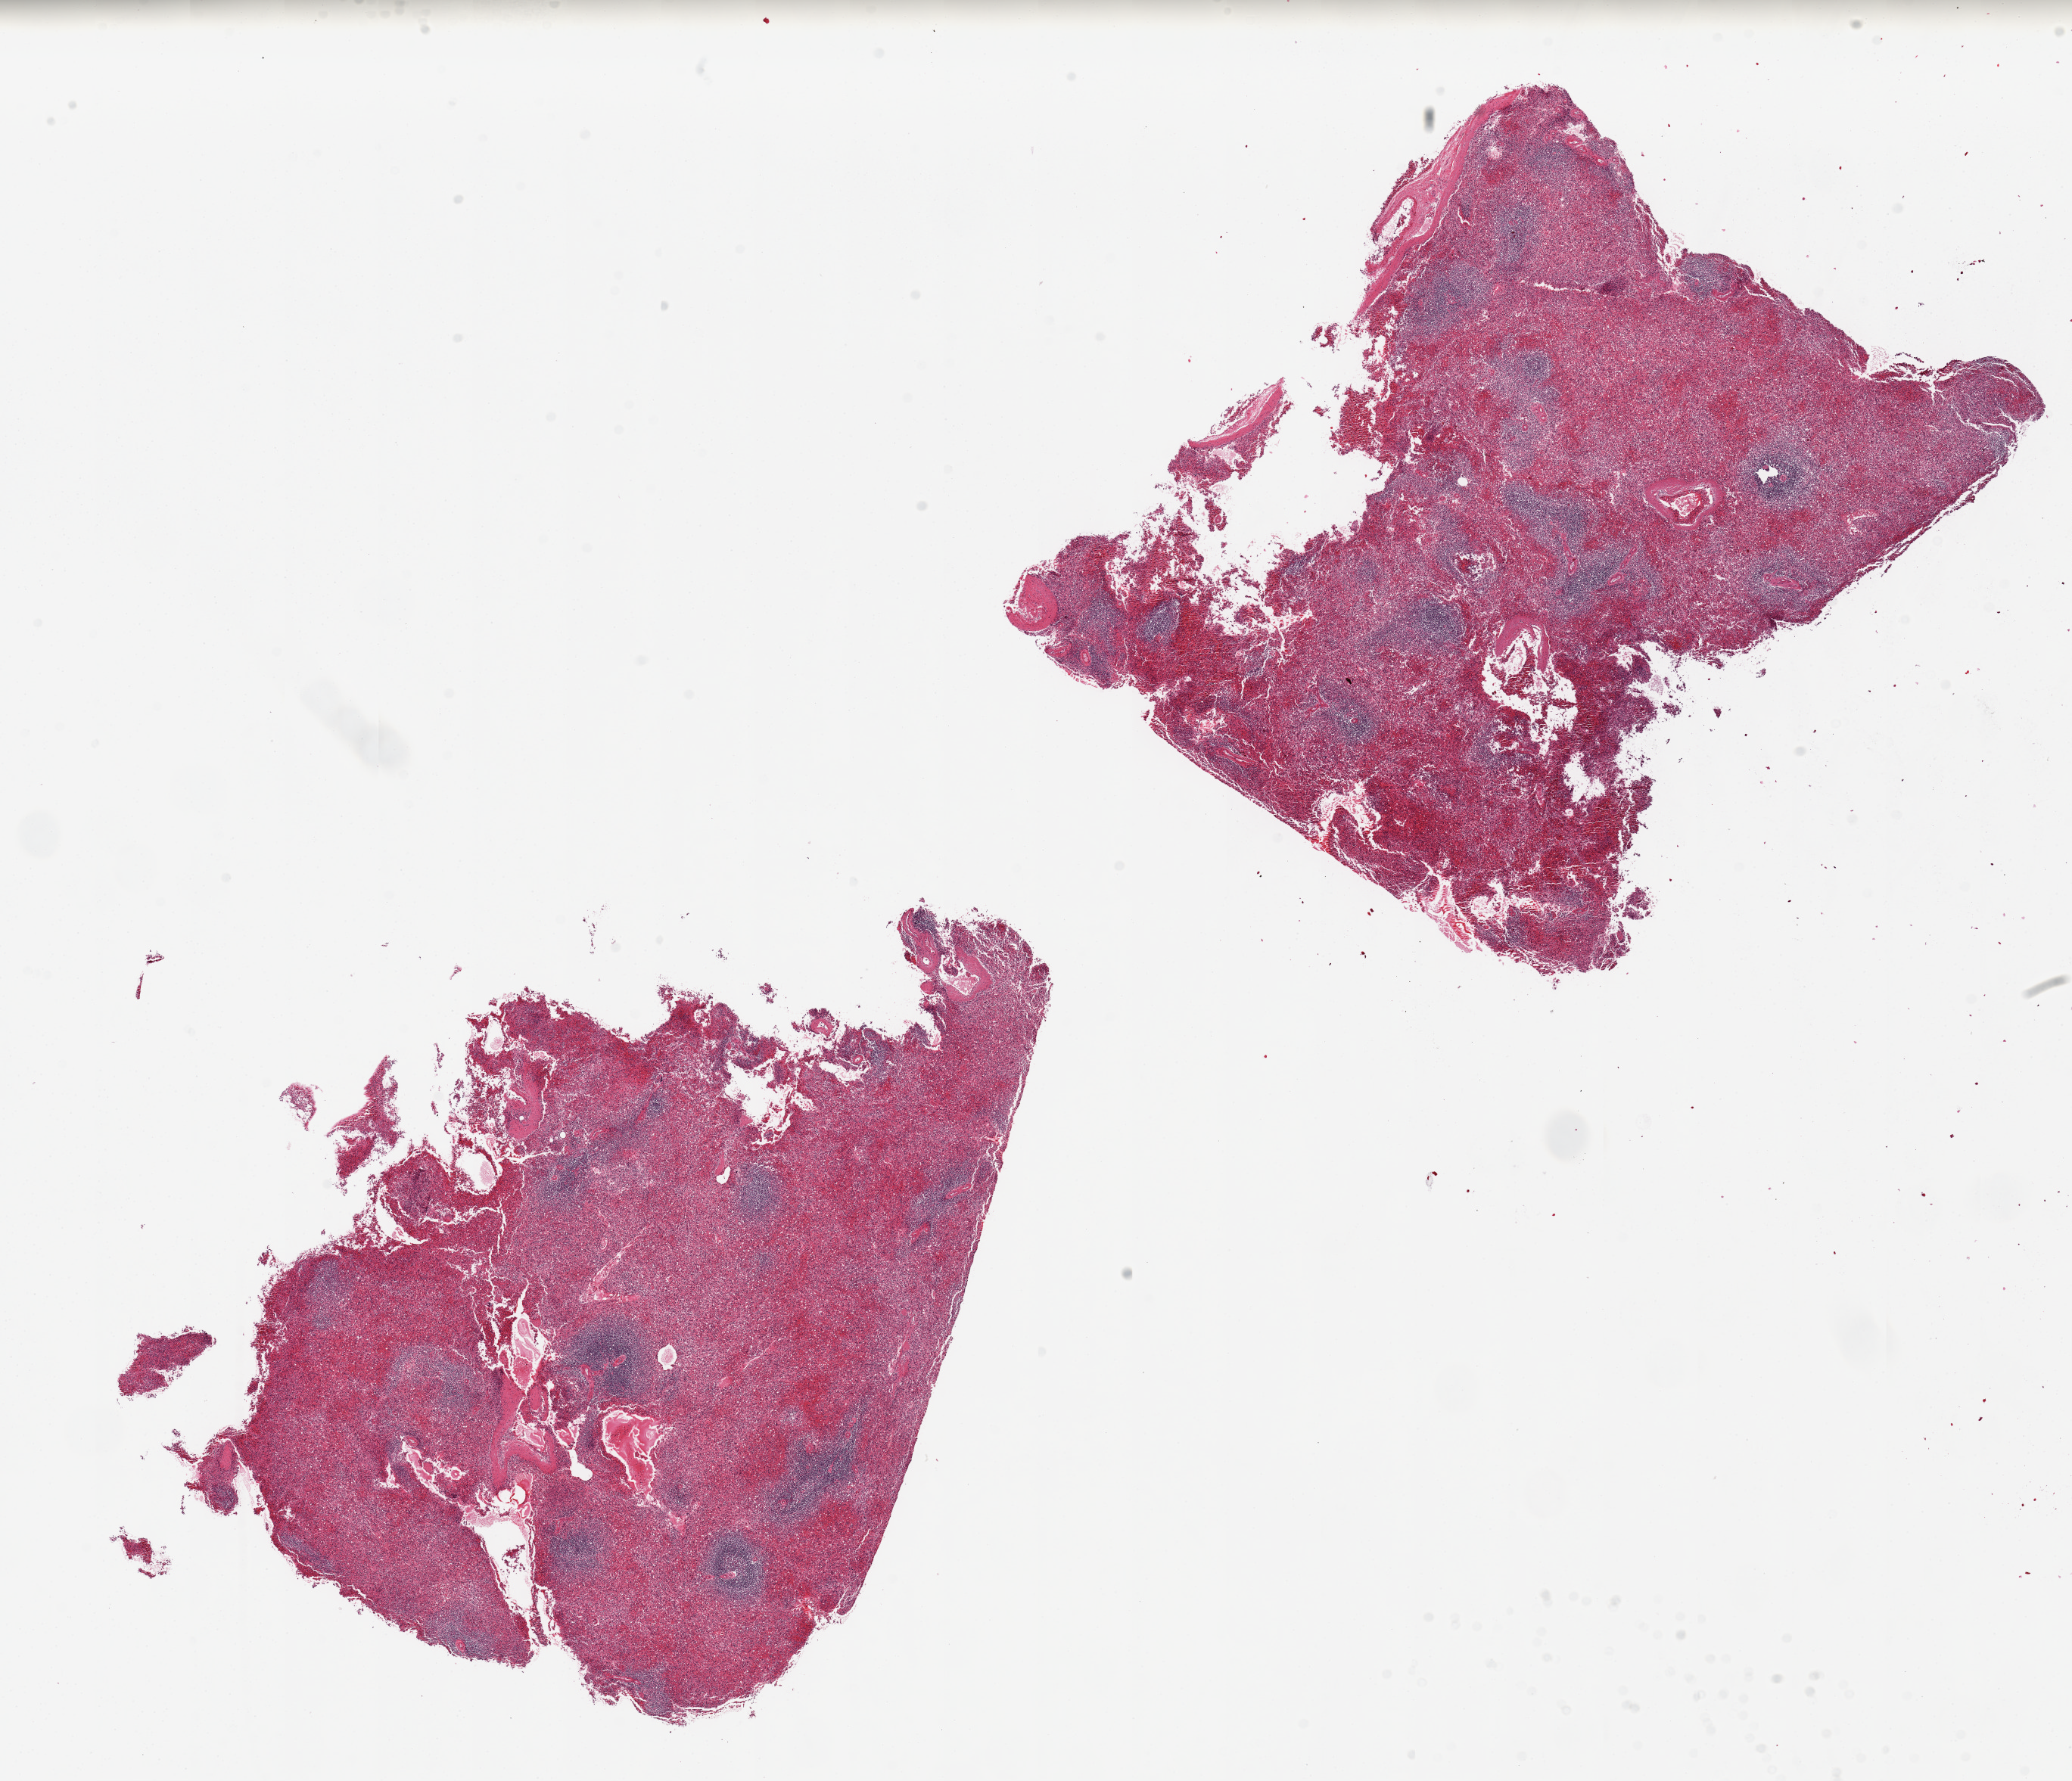
H&E whole-slide image — low-resolution overview of the scanned area, about 21.7 x 18.6 mm (acquisition: 20x scan). PAXgene-fixed, paraffin-embedded tissue. Sampled site (target tissue): spleen. Tissue donor sample. Donor sex: female.
- review note (as recorded): 2 pieces, moderate congestion/autolysis